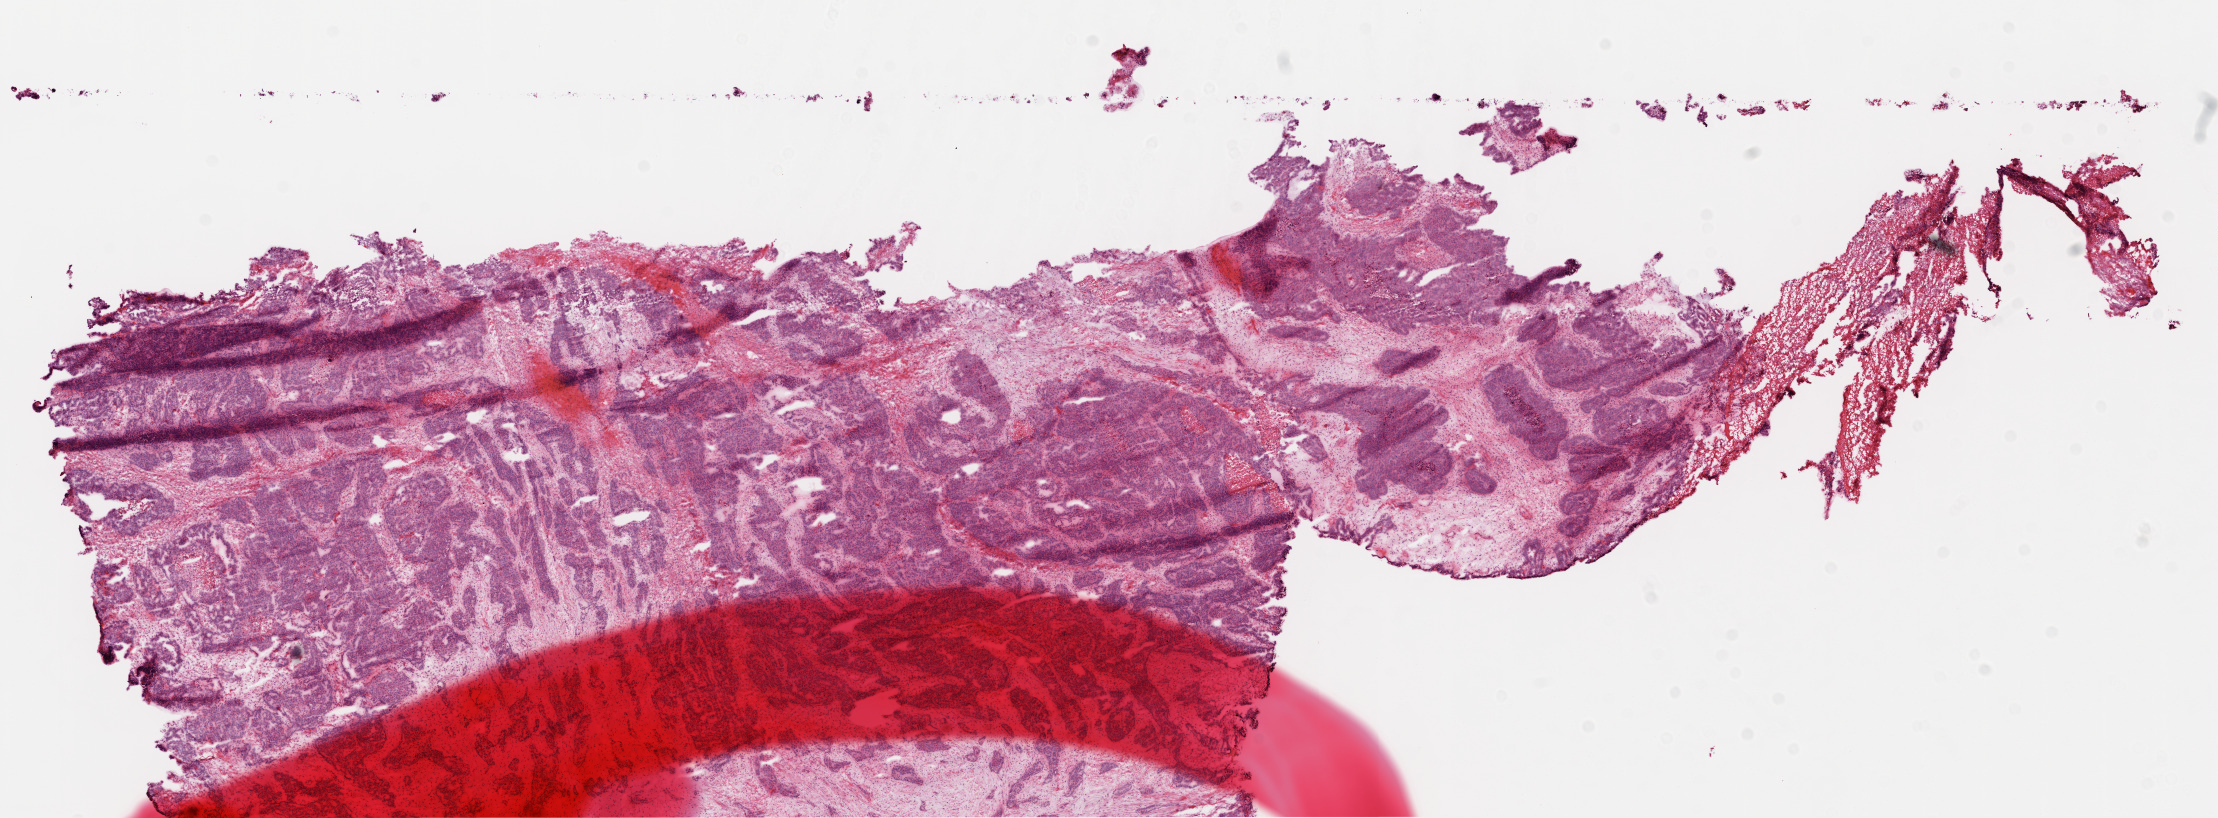
H&E whole-slide image — low-resolution overview of the scanned area, about 17.9 x 6.6 mm (from a 20x scan); frozen section from the top of the tissue portion; ovary, primary tumour sample. Female patient; age at initial diagnosis 72 years. Histologic grade: G3 (poorly differentiated). Slide review estimates, as recorded: tumour cells 70%, tumour nuclei 80%, normal cells 20%, stromal cells 0%, necrosis 10%.
• laterality: bilateral
• FIGO stage: IIIC
• diagnosis: Serous cystadenocarcinoma, NOS